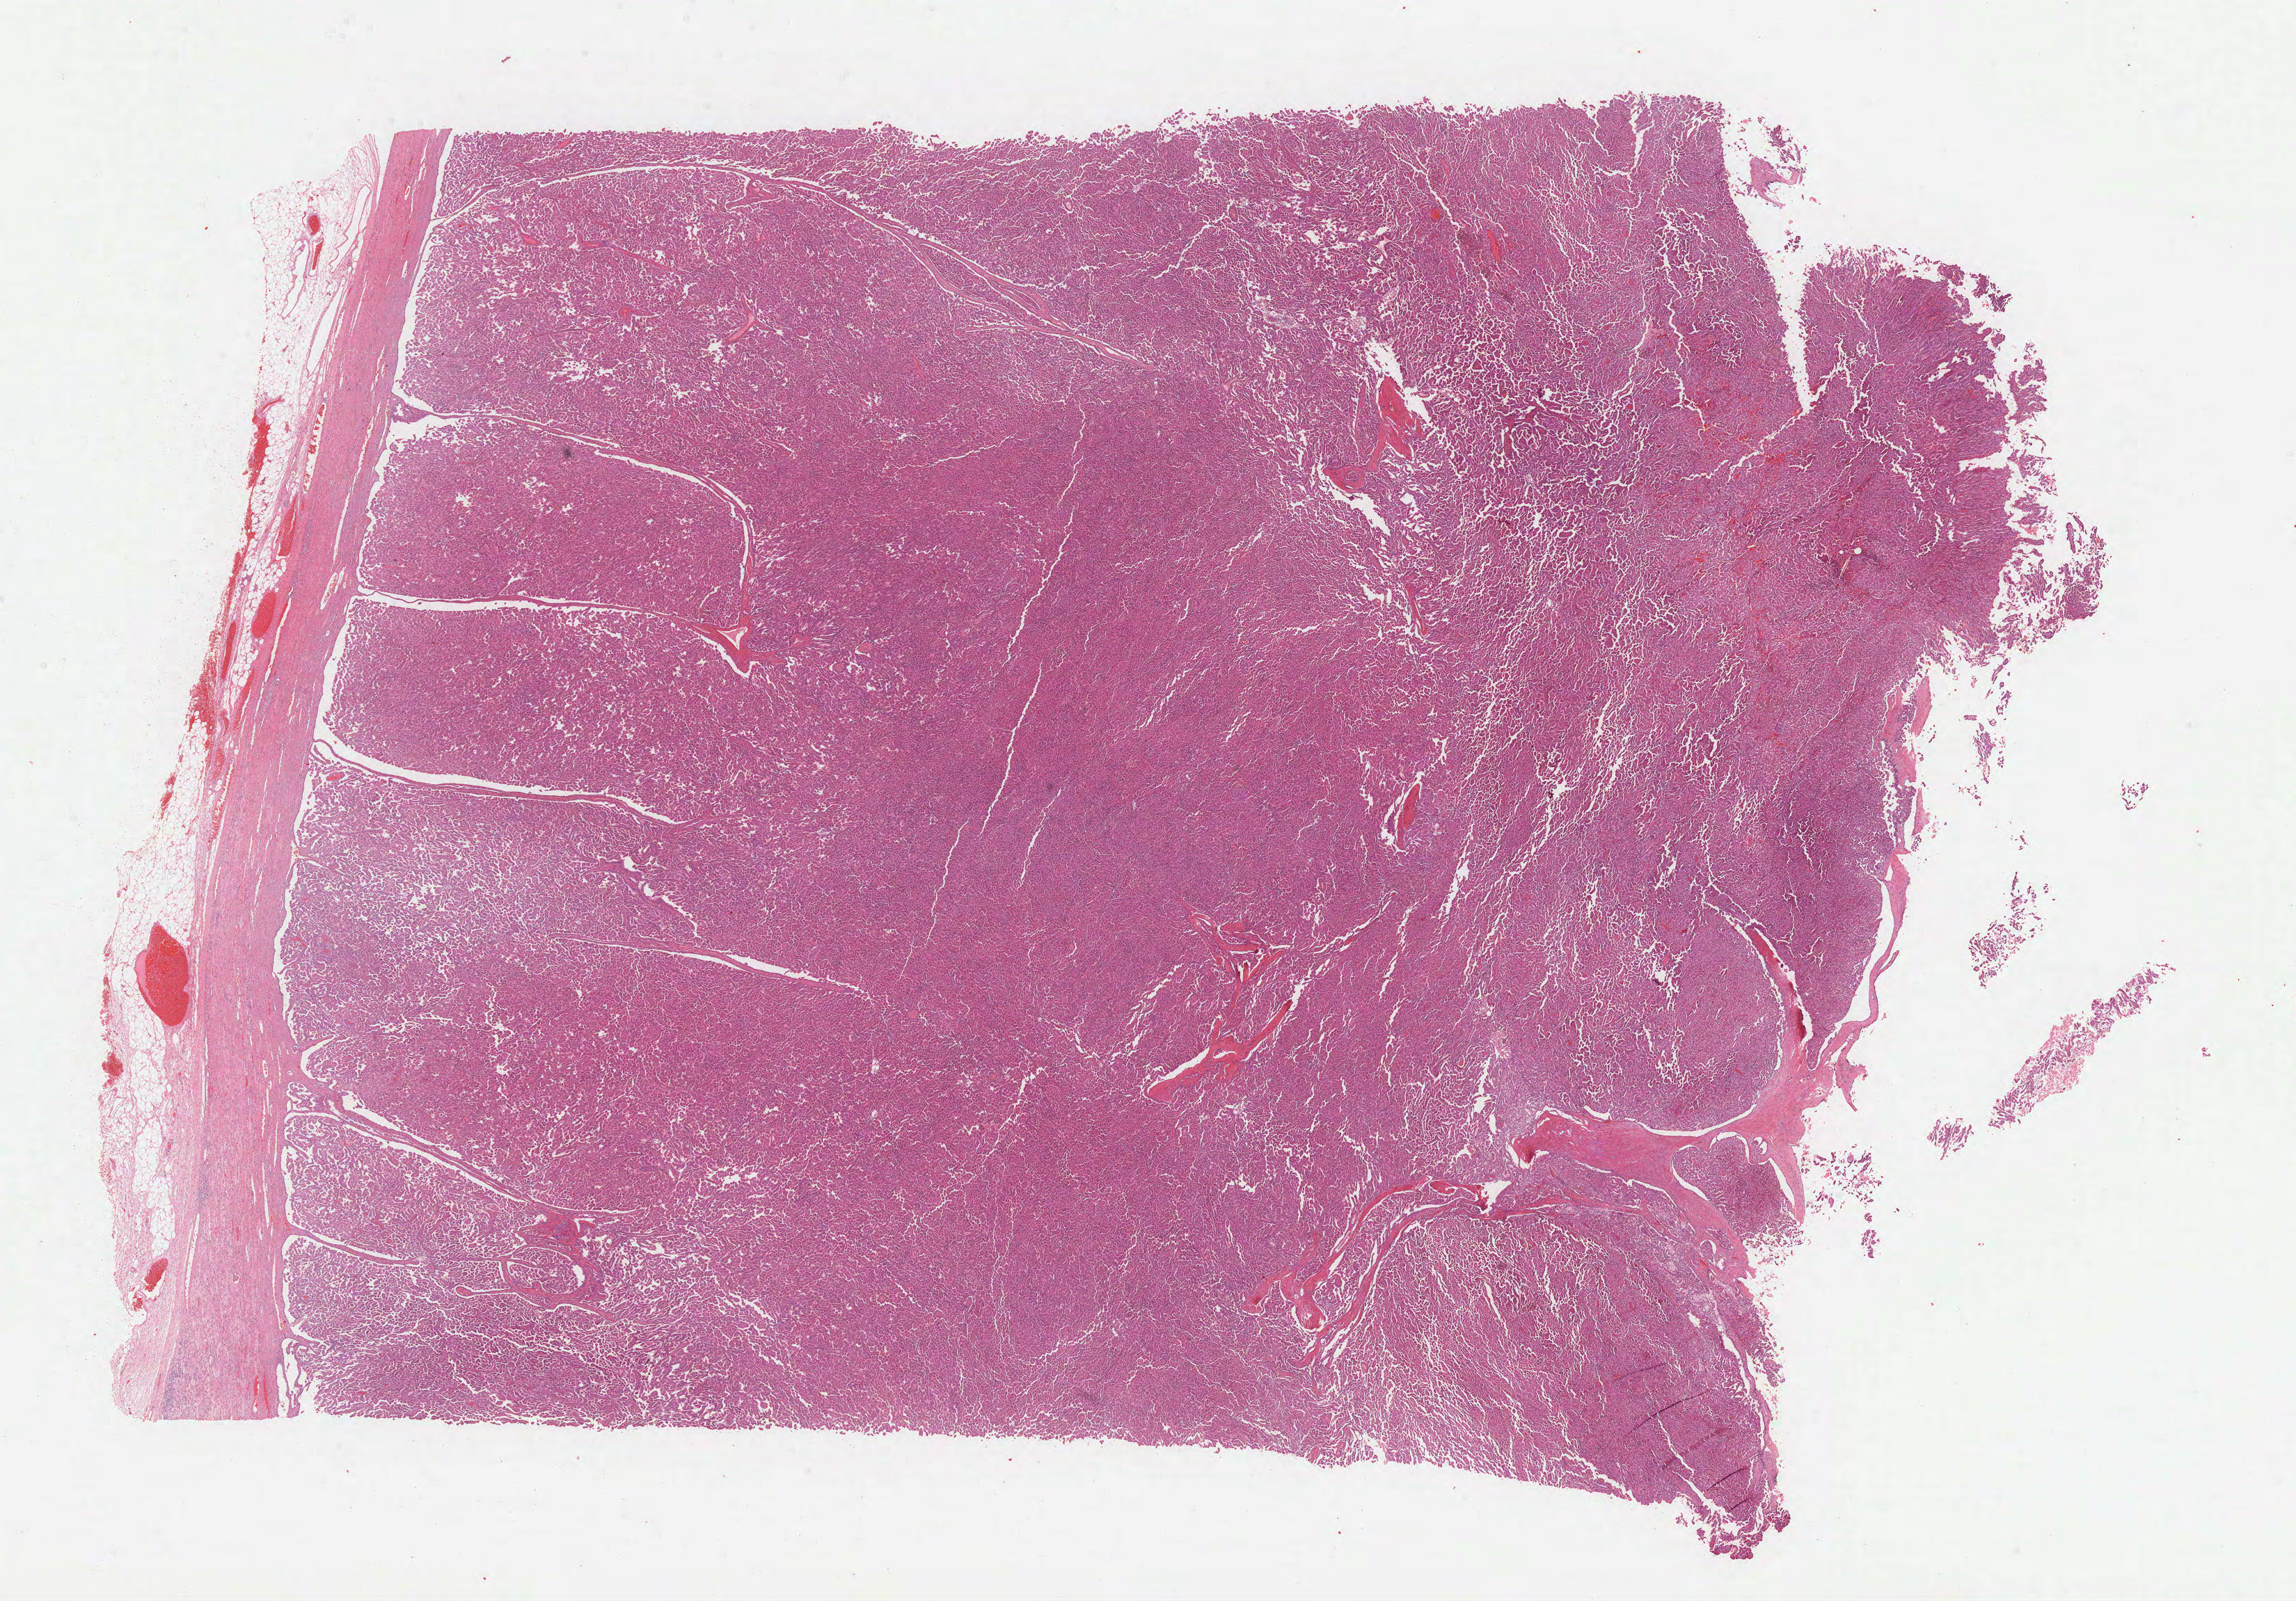
H&E-stained whole-slide image — a low-resolution overview of the entire scanned area, about 26.6 x 18.6 mm, FFPE section, primary tumour sample from the kidney. Male patient; age at initial diagnosis 67 years.
Diagnosis: Papillary adenocarcinoma, NOS.